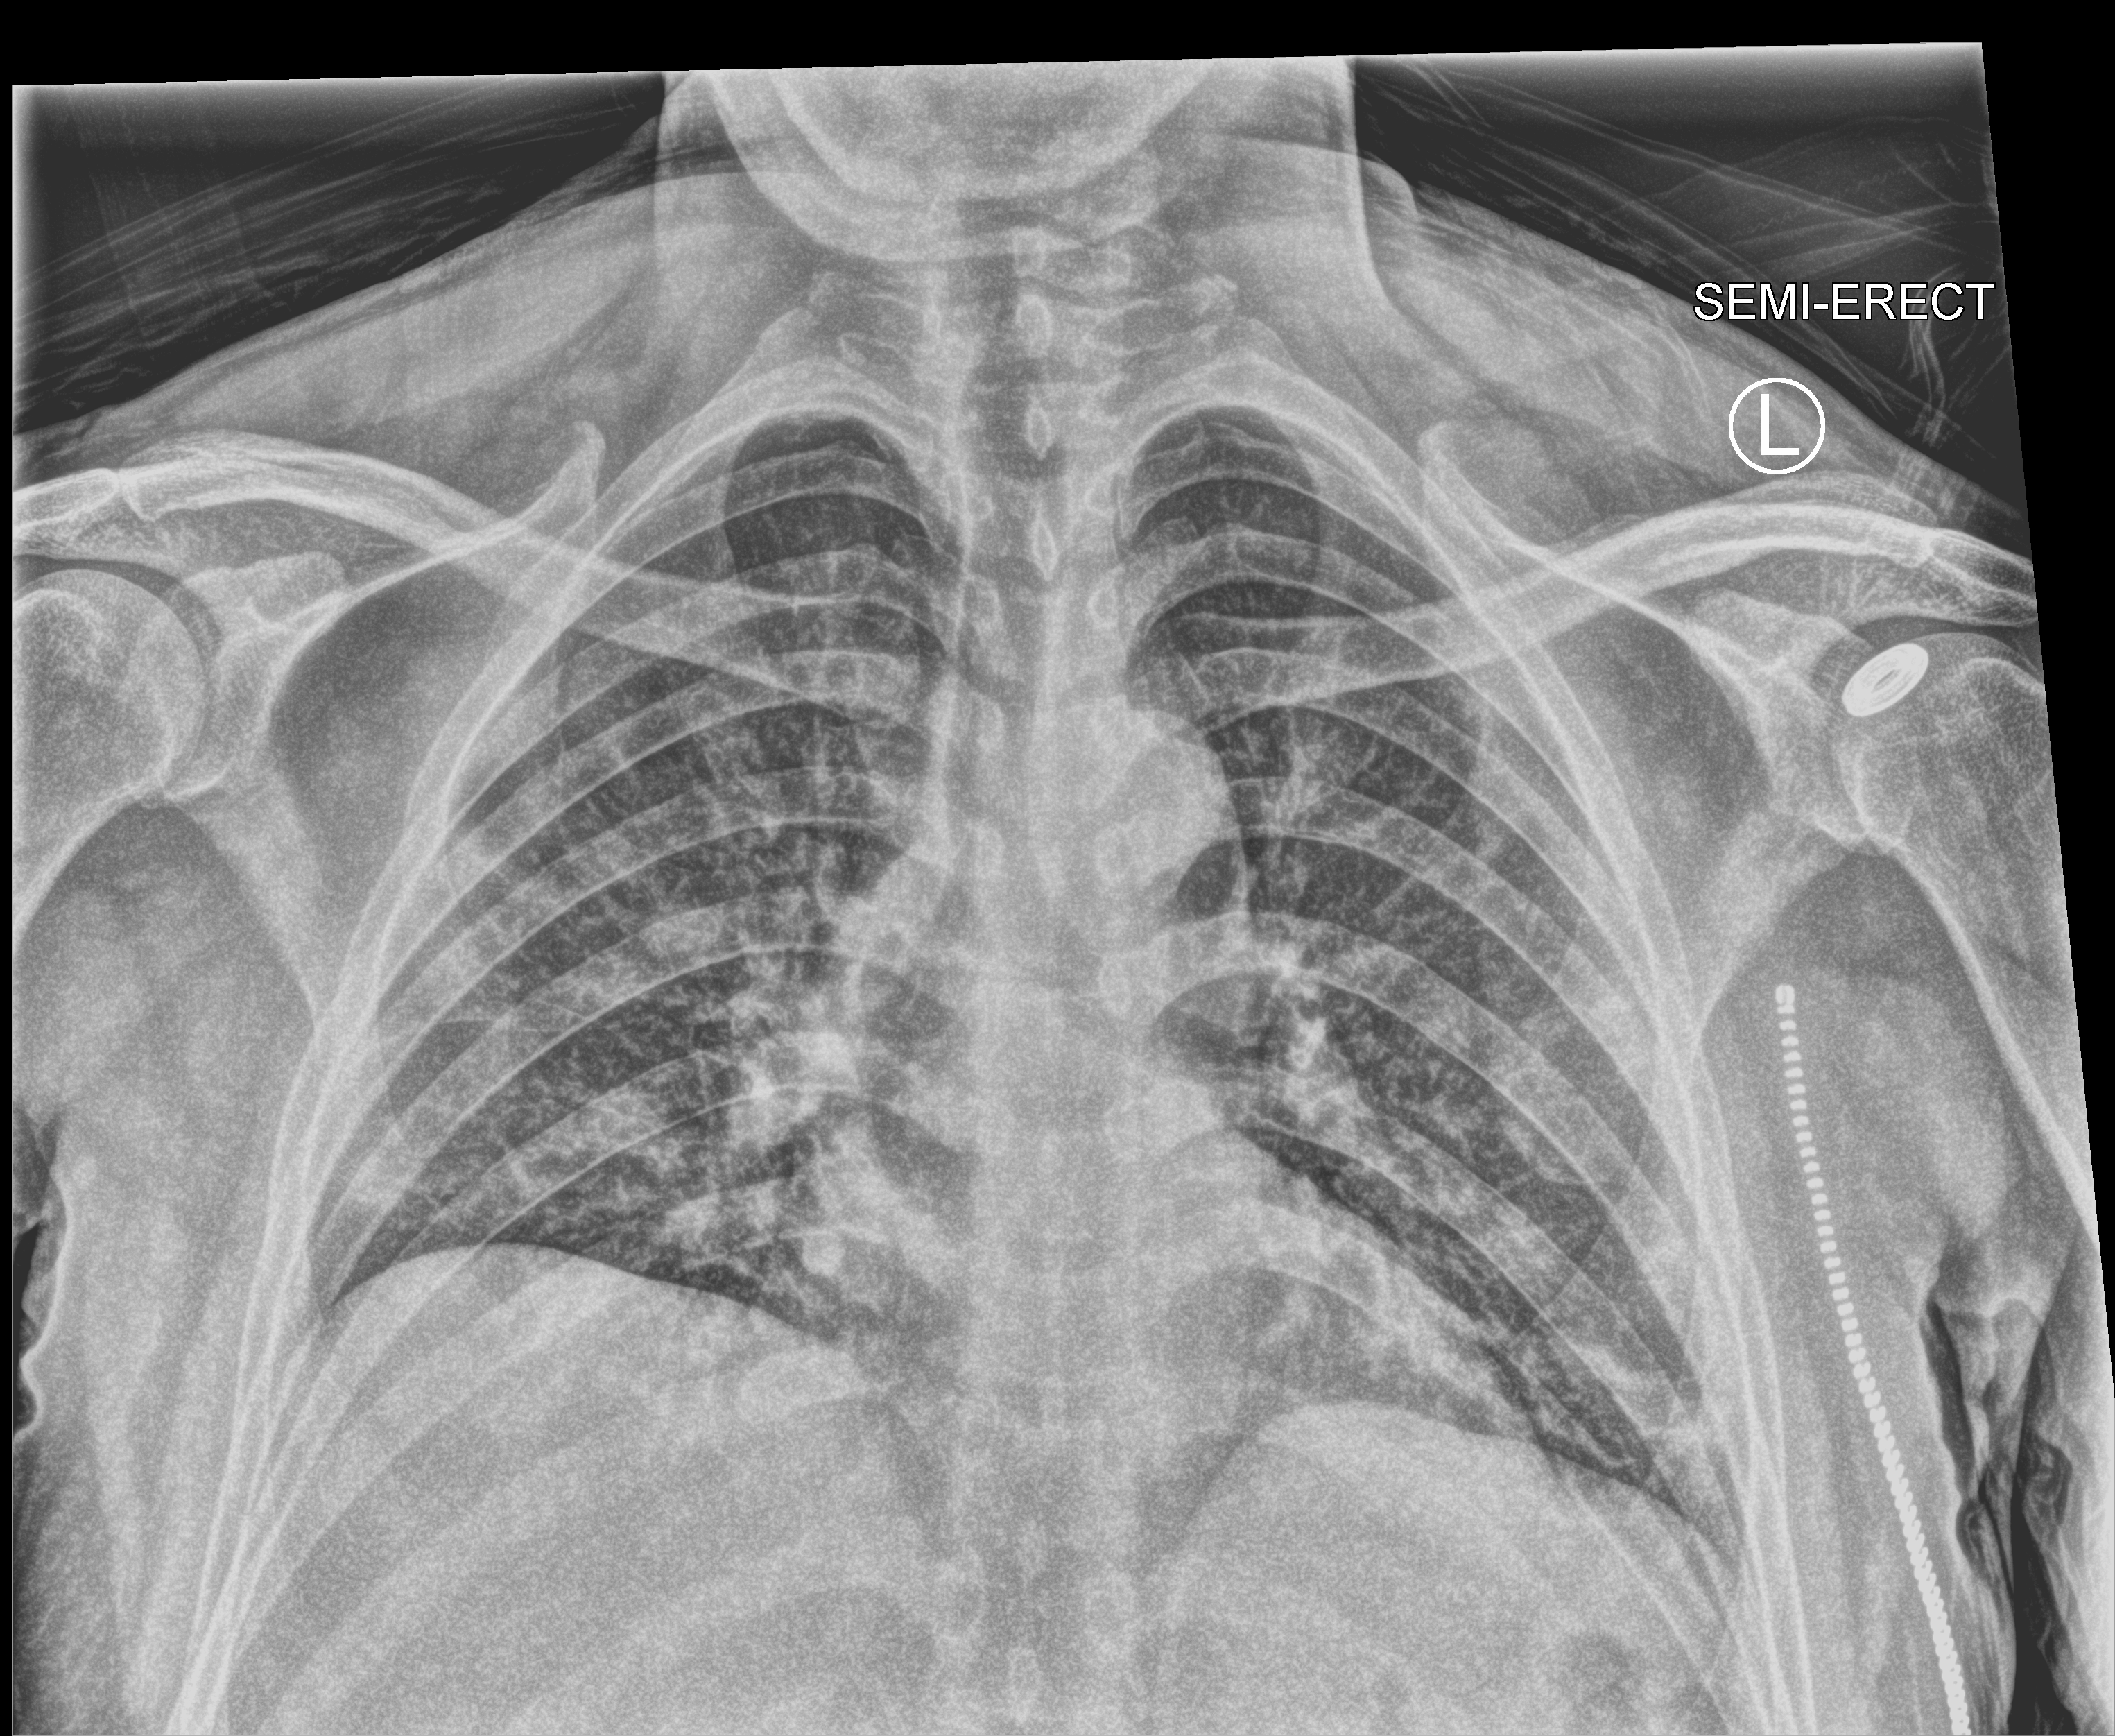
Chest X-ray (portable). Patient hospitalised with COVID-19; male, aged 18–59 years.
From the hospital-stay record, not from the radiograph (when in the stay this image was taken is not recorded): admitted to intensive care during this hospital stay: no; diabetes (admission record): no; COPD (admission record): no.